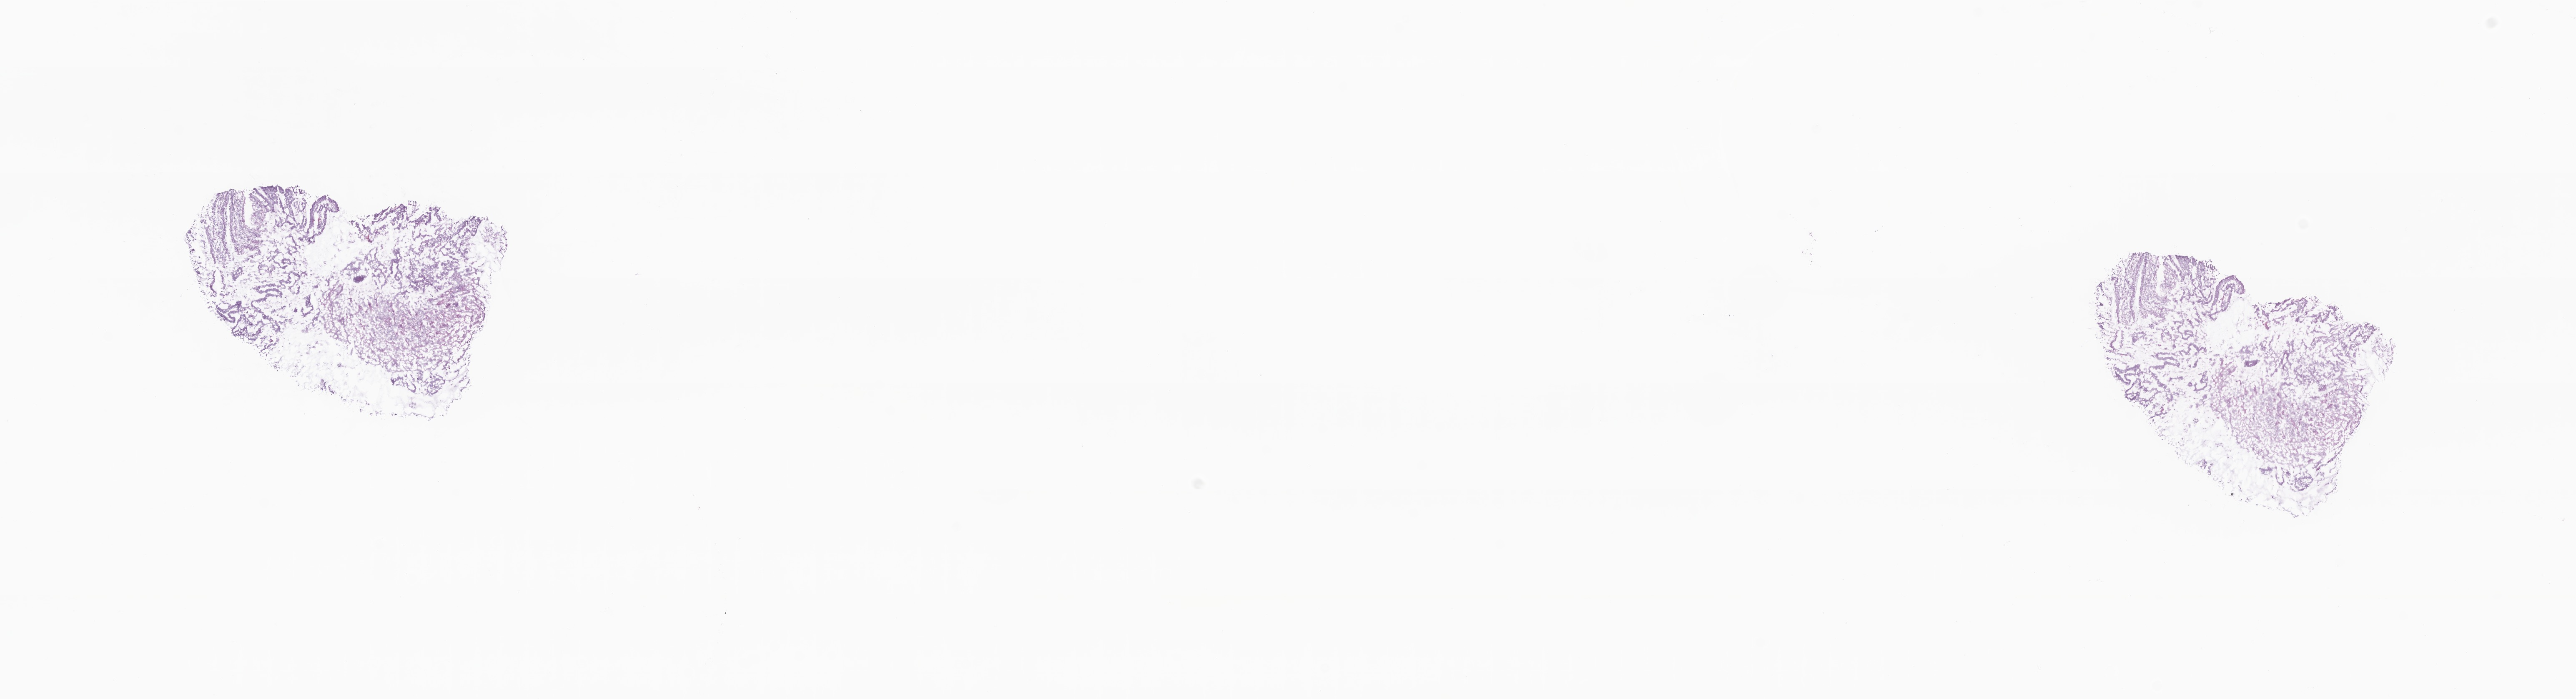
Whole-slide image, H&E stain, whole scanned area (about 26.1 x 7.1 mm) shown as a low-resolution overview; frozen section (tissue freezing medium); specimen: primary tumor; anatomic site: sigmoid colon. Male, age 69 years at initial diagnosis. Slide review estimates, as recorded: tumor cells 75%, tumor nuclei 75%, stromal cells 18%, necrosis 0%, normal cells 7%. Infiltration values recorded for this section: lymphocyte infiltration 5%, monocyte infiltration 2%, neutrophil infiltration 6%.
- section: bottom of the tissue portion
- diagnosis: Adenocarcinoma, NOS